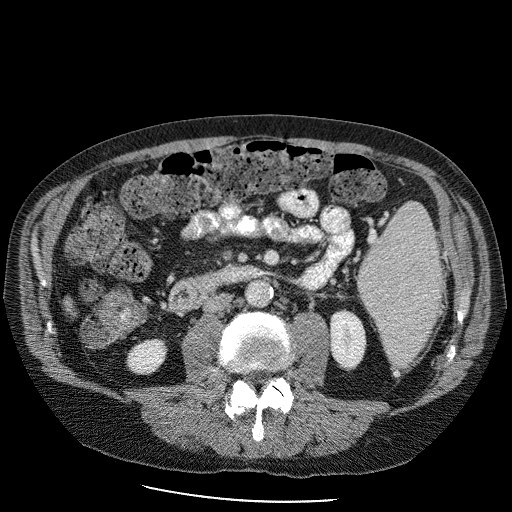
Contrast-enhanced abdominal CT (liver protocol), one axial slice. Slice 19 of 98 in the series (ordered by position). Reconstruction kernel STANDARD. 120 kVp. Soft-tissue window (W 400 / L 40 HU). 2.5 mm slice thickness. 512 × 512 image matrix. From the clinical record (not read from this slice): diagnosis: hepatocellular carcinoma (patient treated with transarterial chemoembolisation; whether this scan precedes or follows treatment is not stated here); TNM stage (as recorded): Stage-II; Child-Pugh class: B; tumour differentiation: moderately differentiated; tumour nodularity: uninodular.
Structures marked on this image (semi-automatic segmentation, software-assisted and operator-edited):
- liver parenchyma outside the tumour (the mass and vessels are separate outlines, so this box may not span the whole liver): bounding box (x1, y1, x2, y2) in pixels: (62, 291, 76, 314)